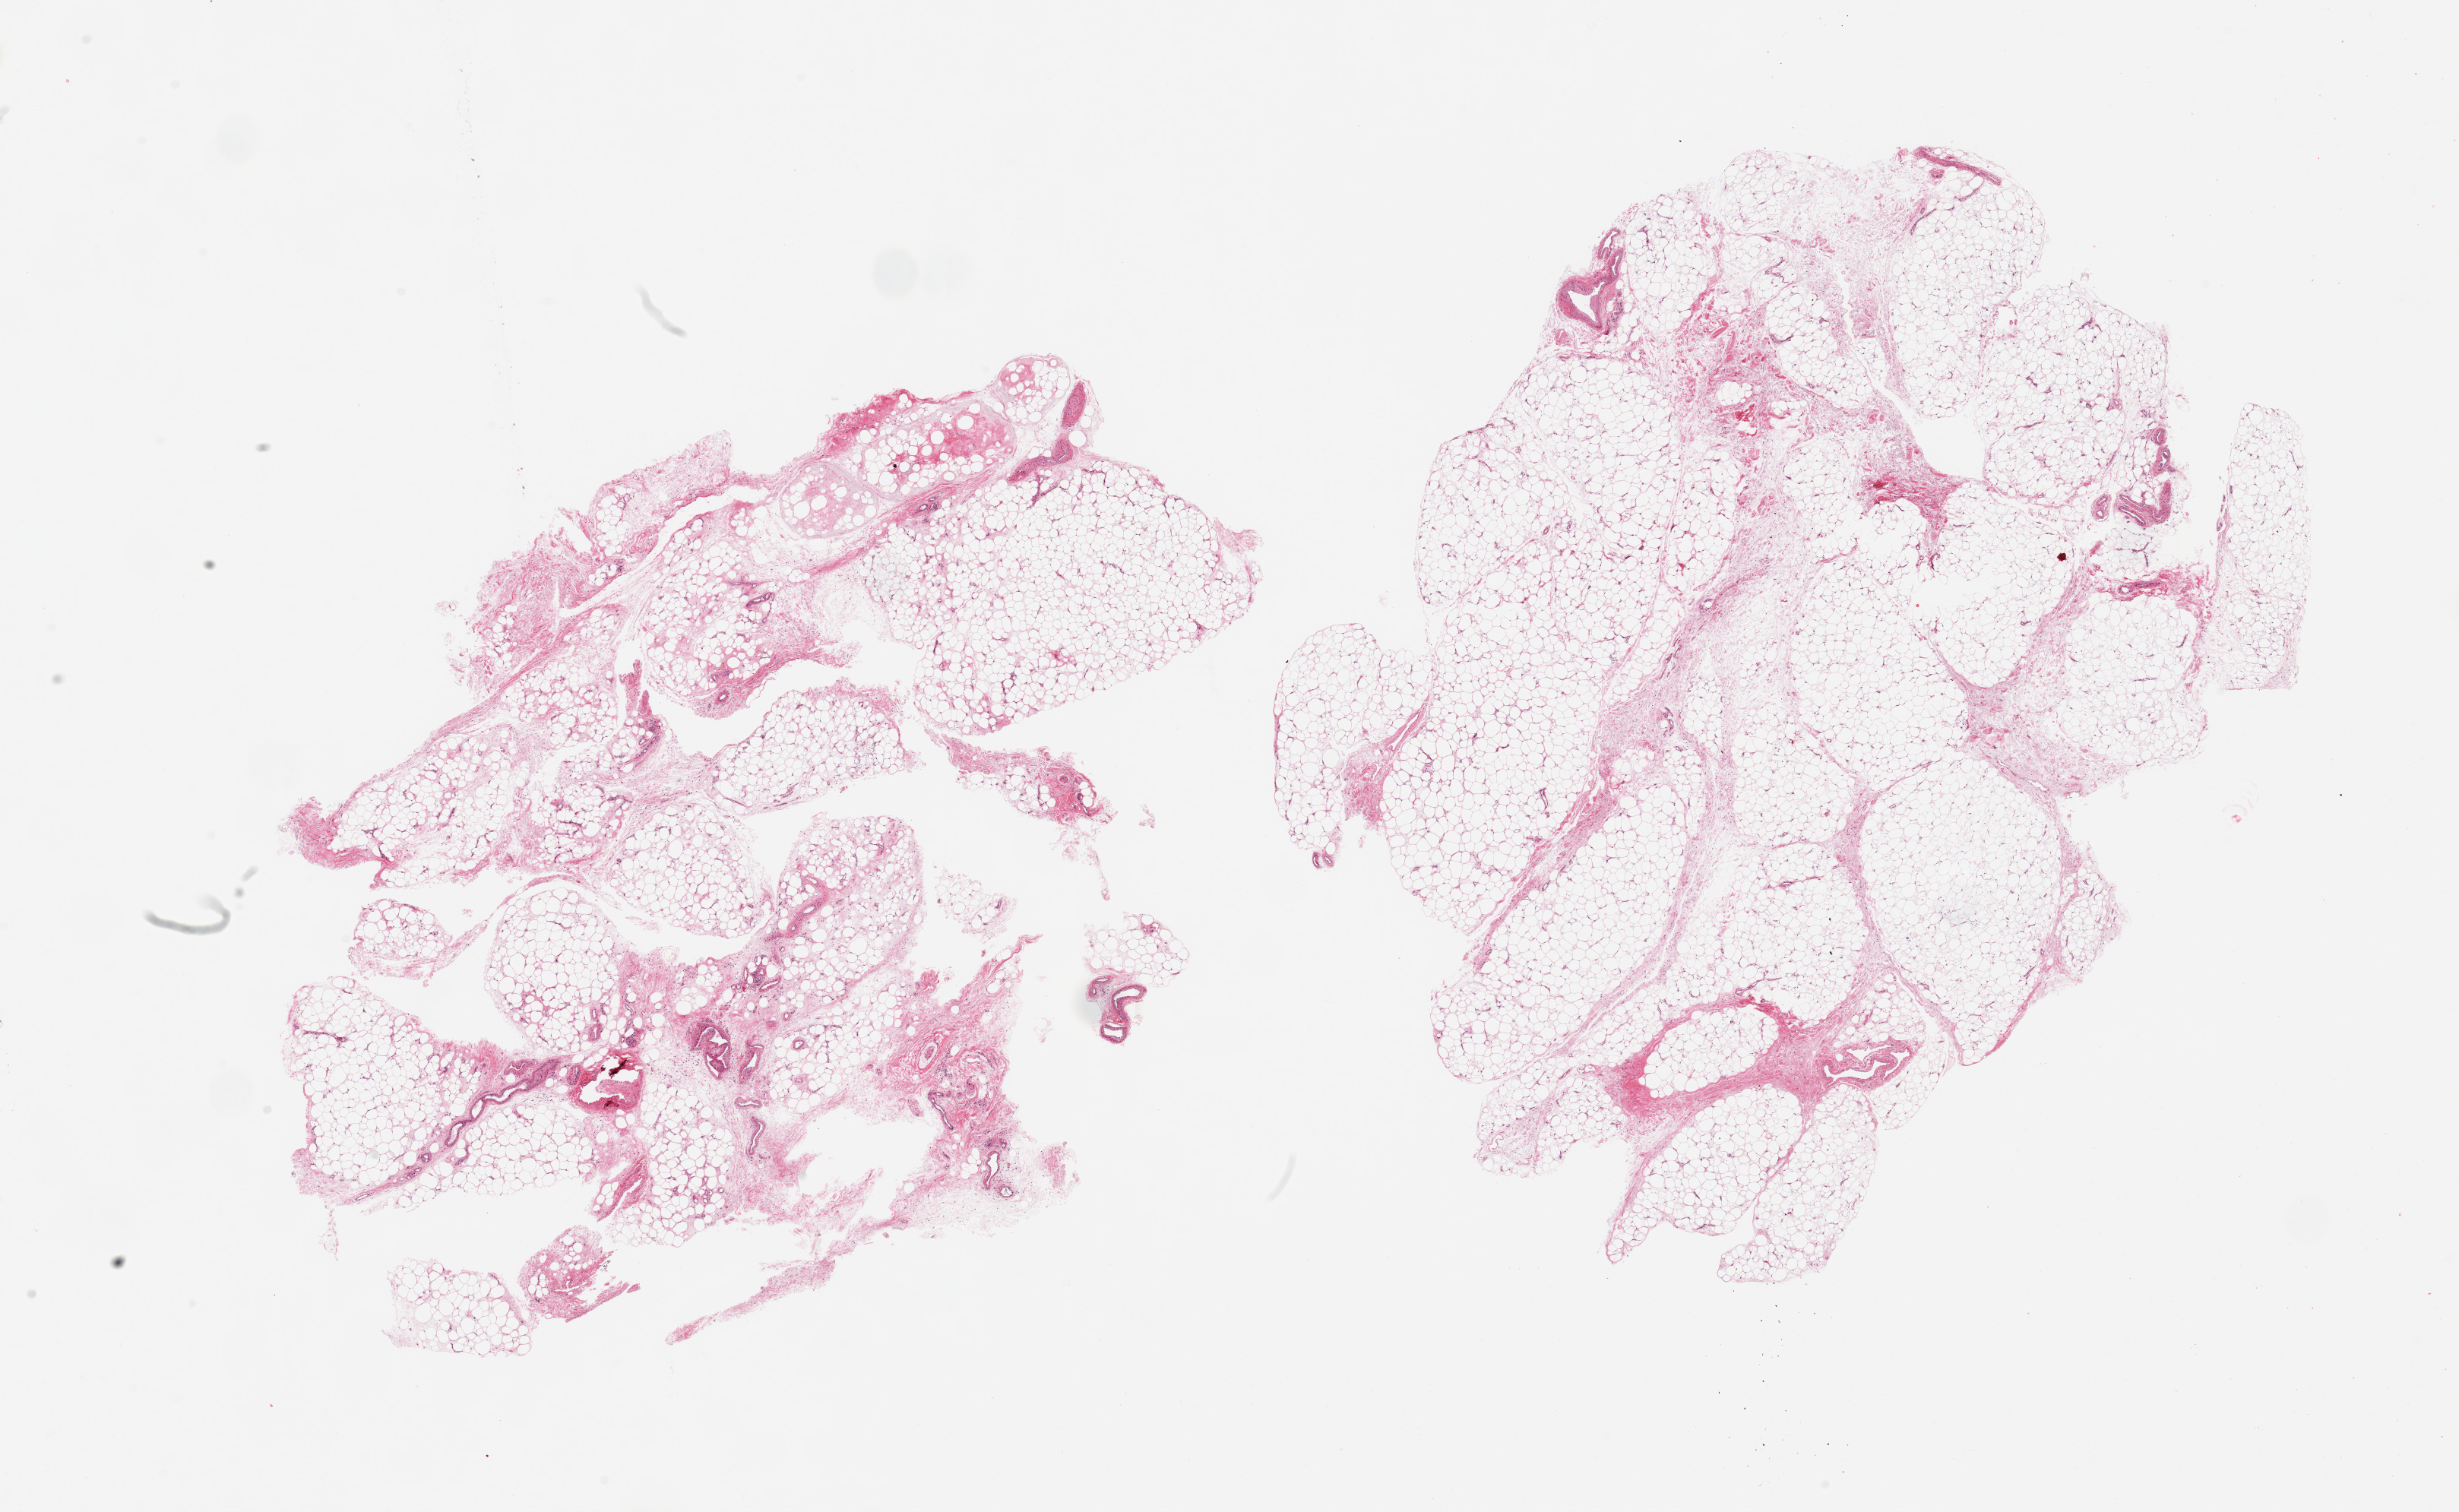
Haematoxylin and eosin whole-slide image, brightfield — low-resolution overview of the scanned area, about 25.6 x 15.7 mm (slide scanned at 20x), PAXgene-fixed, paraffin-embedded tissue, target tissue: adipose tissue, donor tissue sample. Donor: male.
Reviewer comment on this tissue sample: 2 pieces, fascia/vascular elements are ~30% of tissue.